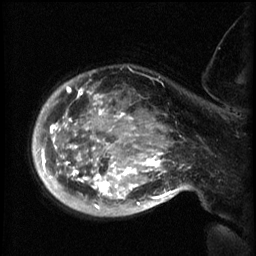
Breast MRI (dynamic contrast-enhanced), one sagittal slice; slice 47 of 60 in the series (ordered by position); 3 images stored at this slice position (order not interpretable as contrast timing); 1.5 T; TE 4.2 ms, TR 8.2 ms; 256 × 256 image matrix. Patient: female, 50 years.
Outlined on this slice (semi-automatically segmented with operator editing):
- analysis volume of interest (the breast-tissue region the enhancement analysis was run in; not a lesion): bounding box <50,70,169,217> (left, top, right, bottom; pixels)
- tumour enhancement mask (voxels above the 70 % enhancement threshold inside the analysis volume of interest): <50,84,169,209>